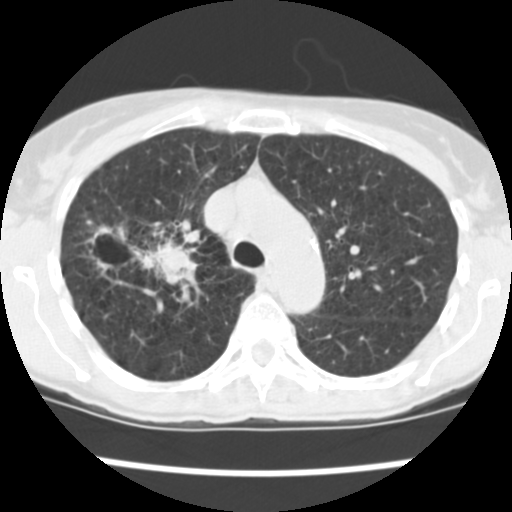
Low-dose screening chest CT, one axial slice. Position 176 of 252 along the scan axis. Reconstruction kernel STANDARD. Lung window (W 1500 / L -600 HU). 512 × 512 image matrix.
Structures marked on this image (expert manual segmentation):
- lesion 2 (tumor, lower lobe of right lung): bounding box <132,222,198,288> (left, top, right, bottom; pixels)